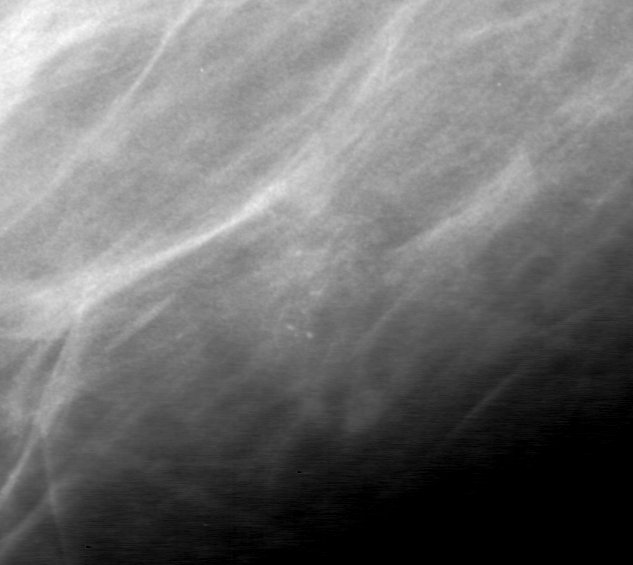
Cropped region of a digitized screen-film mammogram centred on a radiologist-marked abnormality; right breast; MLO view; BI-RADS breast density category 2 (scale 1–4).
- Calcifications, morphology punctate, distribution clustered; BI-RADS assessment category 0 (incomplete: needs additional imaging); pathology result (as recorded, not read from the image): benign.